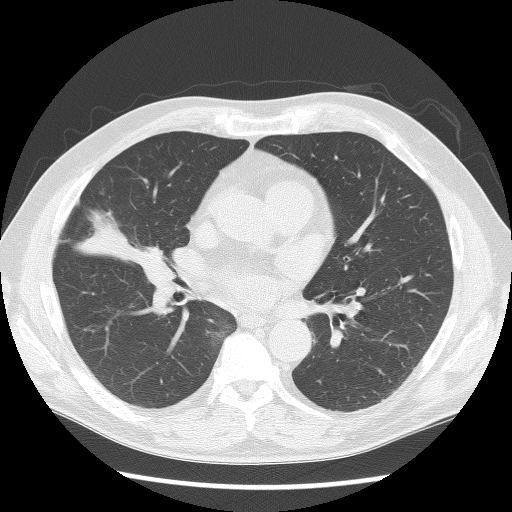
Low-dose screening chest CT, axial slice; third annual screen; lung window (W 1500 / L -600 HU); 2.5 mm slice thickness; lung (sharp) reconstruction kernel (BONE); slice 70 of 146 in the series. Male, age 57 years at enrolment. Former smoker at enrolment.
Expert reader's lesion annotation, bounding box (x1, y1, x2, y2) in pixels: (138, 252, 176, 288). The exam's reader record, not a measurement of the box and not confirmed to be the same lesion: non-calcified nodule or mass ≥4 mm, right middle lobe, 19 × 18 mm, smooth margins, soft tissue attenuation, pre-existing on the prior screen: yes; interval growth: yes. Participant outcome: lung cancer diagnosed 69 days after this screen — carcinoid tumor, NOS, right middle lobe, carcinoid, stage not assessed, 15 mm at pathology.